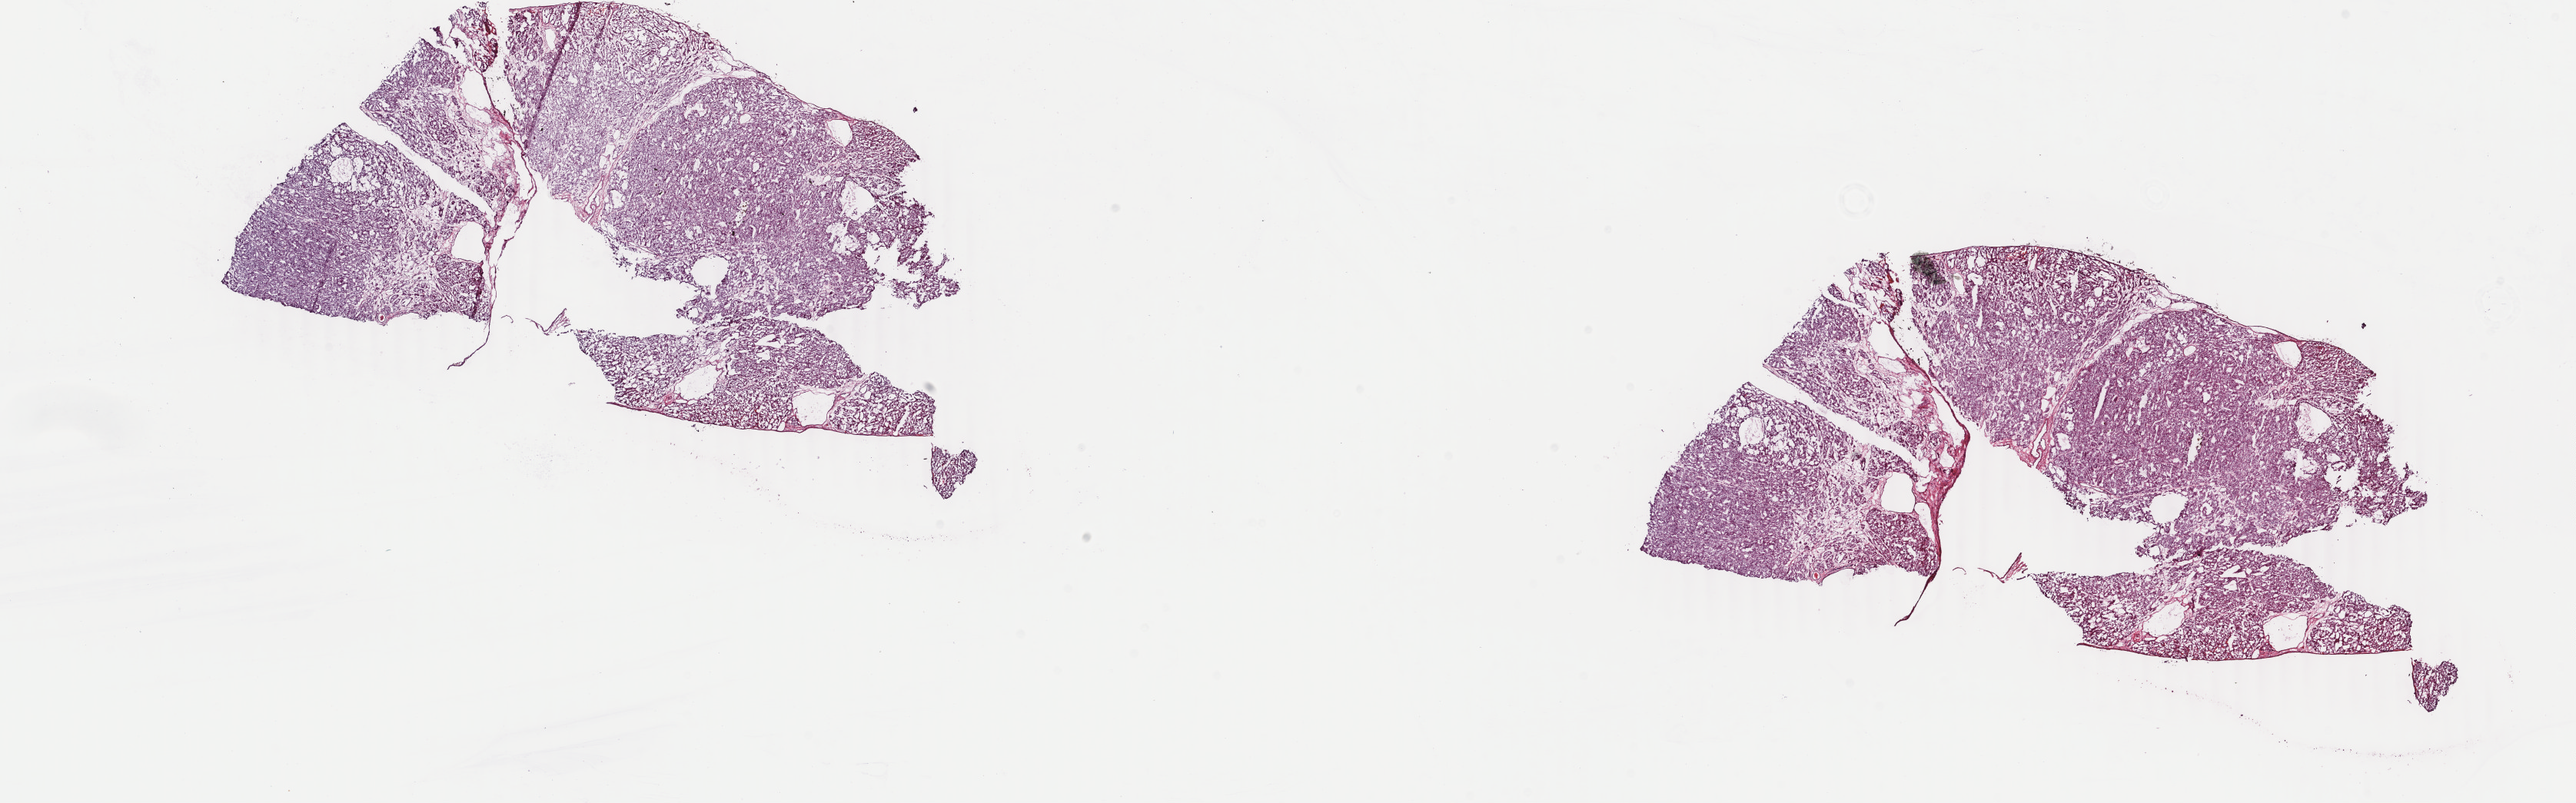
Digitized Hematoxylin and eosin (H&E) stained tissue section (whole slide) — a low-resolution overview of the entire scanned area, about 26.7 x 8.3 mm (acquisition: 40x scan). Frozen section. Primary tumour sample from the kidney. Male, age 74 years at initial diagnosis. Slide review estimates, as recorded: tumour cells 100%, tumour nuclei 80%, normal cells 0%, stromal cells 0%, necrosis 0%. Inflammatory infiltration, as recorded: lymphocyte infiltration 2%, monocyte infiltration 2%, neutrophil infiltration 0%.
Pathologic diagnosis: Renal cell carcinoma, chromophobe type. AJCC pathologic stage: I (7th edition). TNM: T1a NX MX.